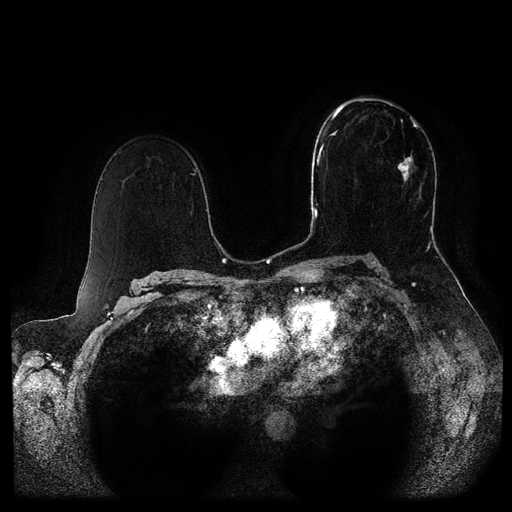
Breast MRI (dynamic contrast-enhanced, multi-phase), one axial slice; slice 60 of 116 in the series (ordered by position); dynamic contrast-enhanced series, time point 2 of 5 at this slice position (early post-contrast); 1.5 T; TE 2.6 ms, TR 5.3 ms; 2 mm slice thickness; 512 × 512 image matrix, field of view 370 × 370 mm. Patient: female, 51 years.
Structures marked on this image (semi-automatically segmented with operator editing):
- breast lesion (labelled 'tumour' in the annotation; benign lesions carry a separate 'benign' label): bounding box [x1, y1, x2, y2] px = [397, 151, 413, 187]